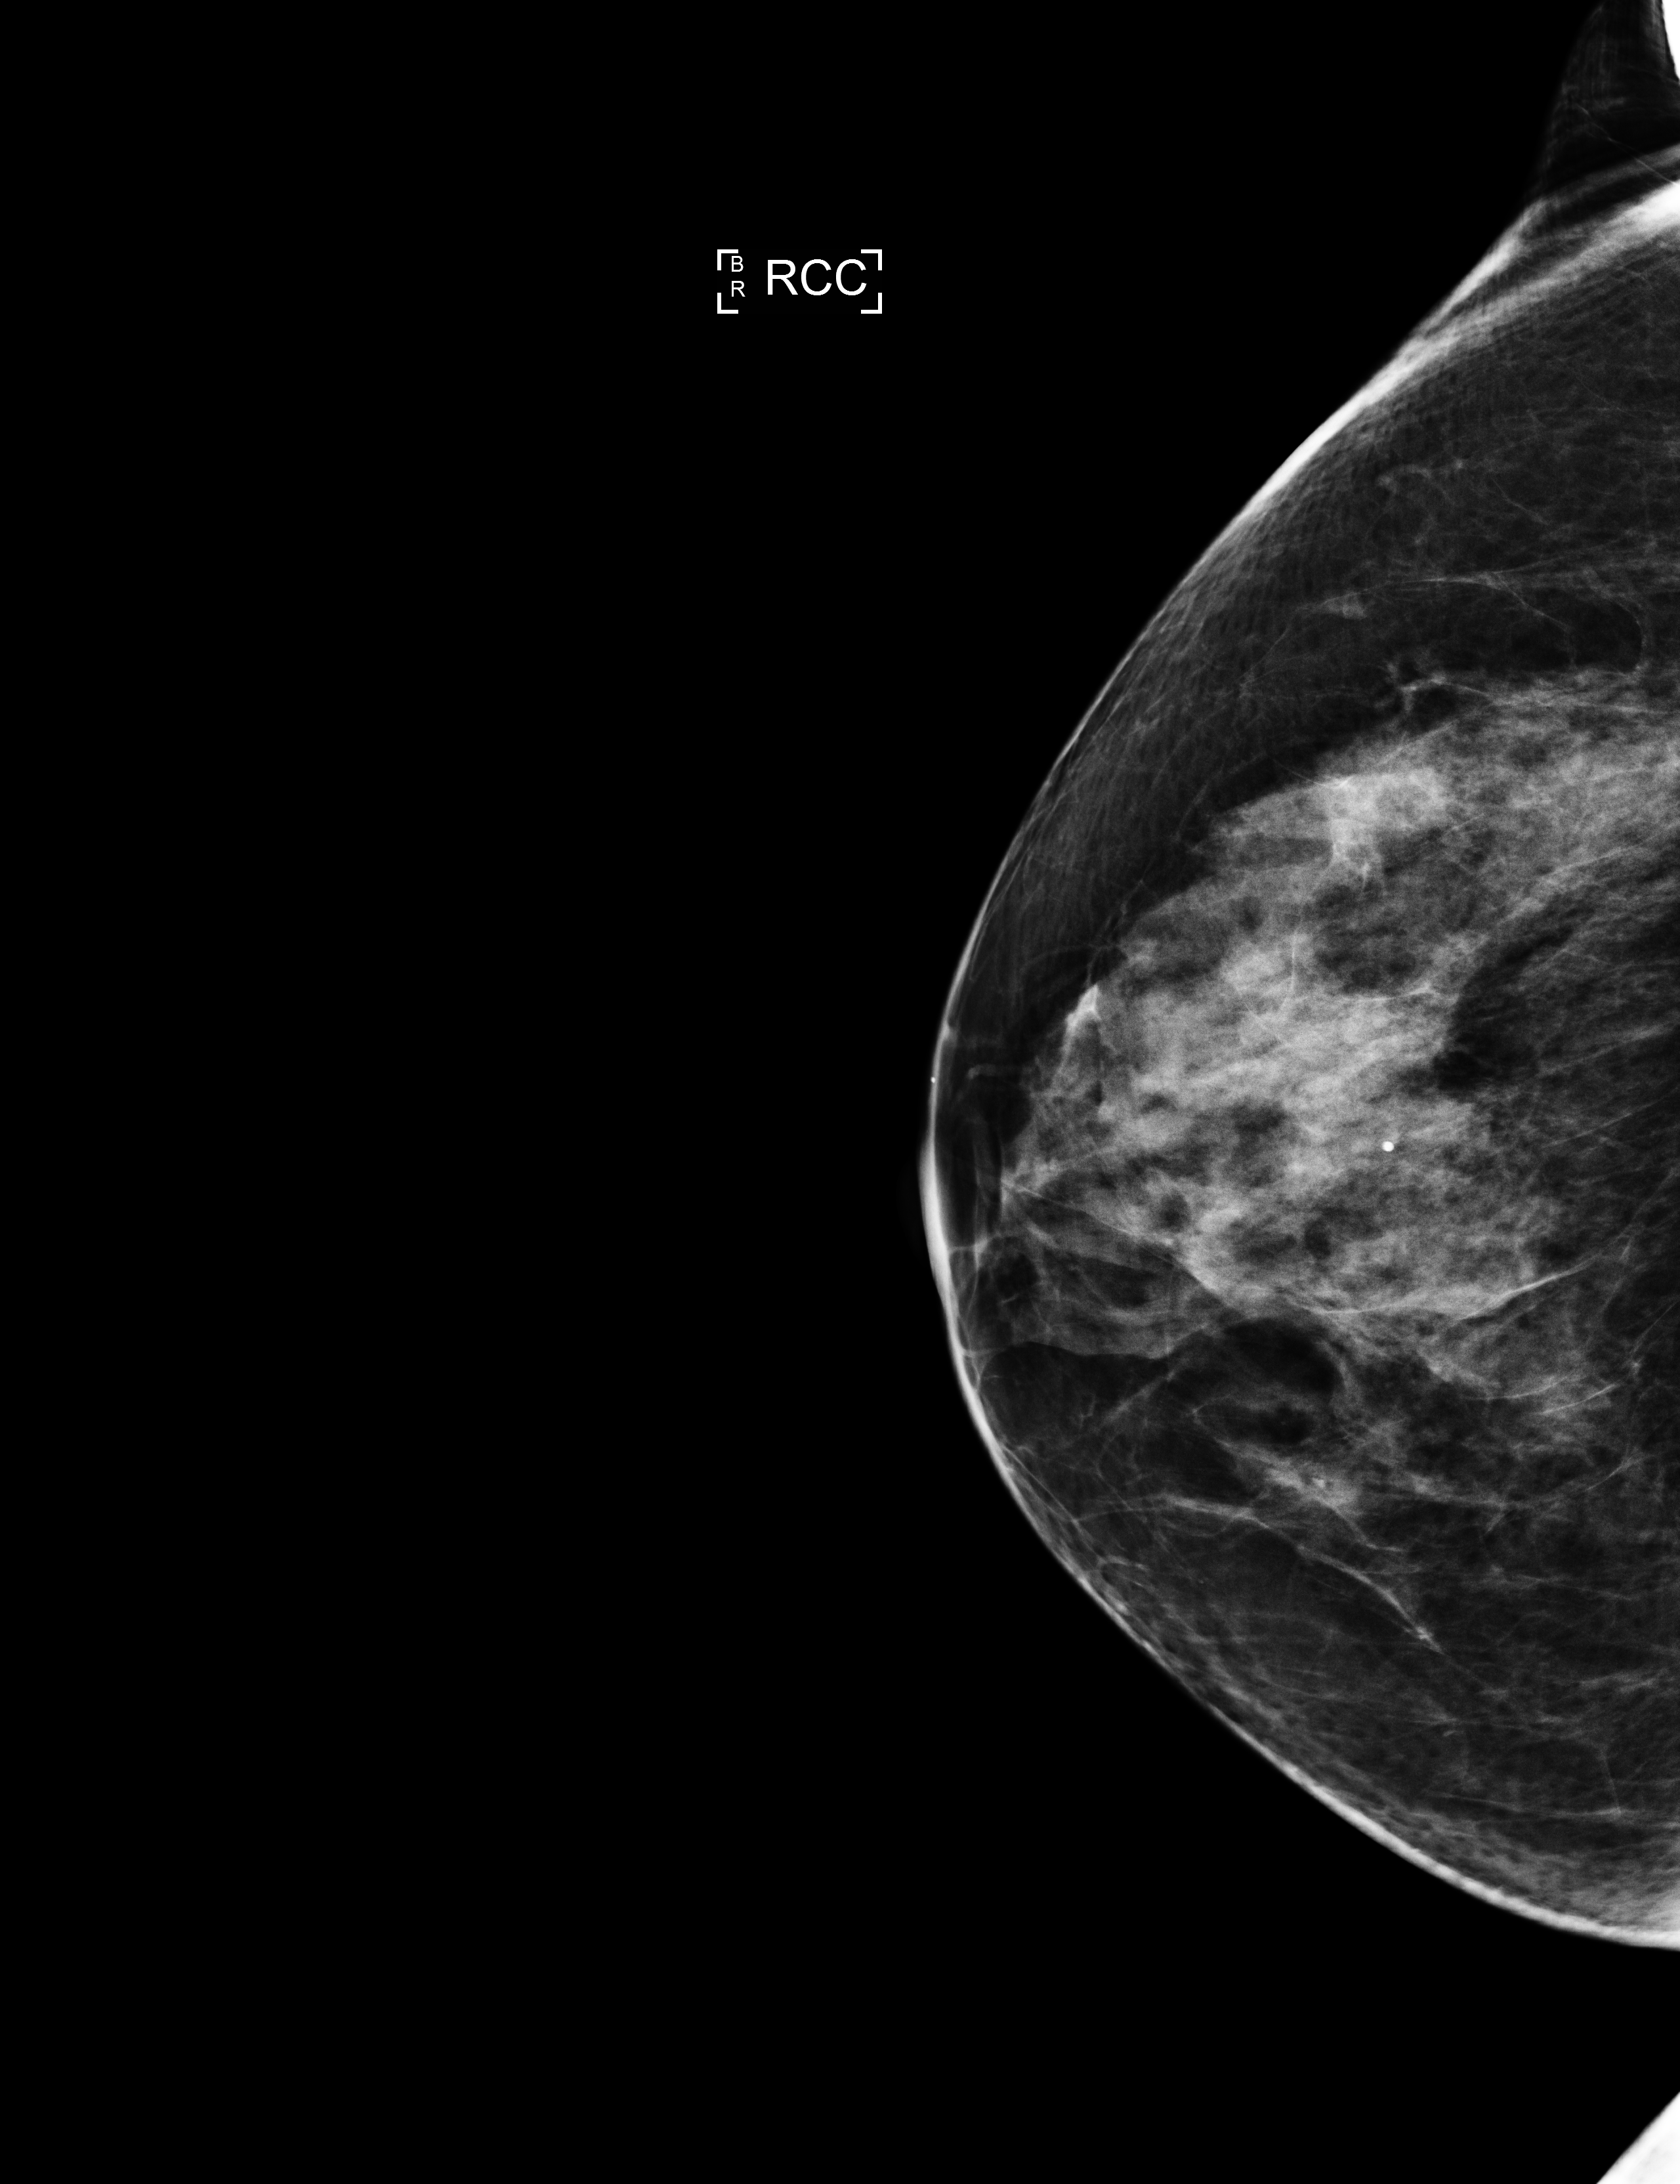
Annual screening mammography examination, compressed breast thickness 60 mm. Patient: female, 67 years.
Image type: full-field digital mammogram. Breast: right. Projection: CC view.